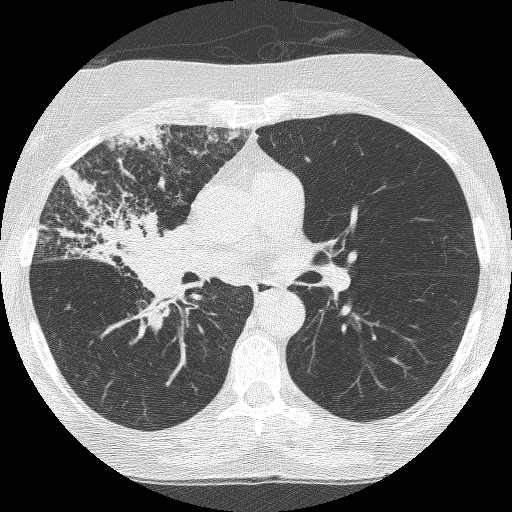
Axial slice from a low-dose chest CT screening exam; third annual screen; lung window (W 1500 / L -600 HU); 1.25 mm slice thickness; lung (sharp) reconstruction kernel (BONE); 512 × 512 image matrix, field of view 294 × 294 mm. Female, age 64 years at enrolment. Former smoker at enrolment.
- Lesion marked by an expert reader, bounding box <66,179,202,316> (left, top, right, bottom; pixels).
- Screening reader's record for this exam (one nodule recorded; not confirmed to be the boxed lesion): non-calcified nodule or mass ≥4 mm, right upper lobe, 49 × 43 mm, spiculated (stellate) margins, soft tissue attenuation, pre-existing on the prior screen: yes; interval growth: yes.
- Official screen result: positive, other.
- Later outcome: lung cancer diagnosed 7 days after this screen — adenocarcinoma, NOS, right upper lobe, right middle lobe, right hilum, stage IV (AJCC 6th edition), 85 mm at pathology.